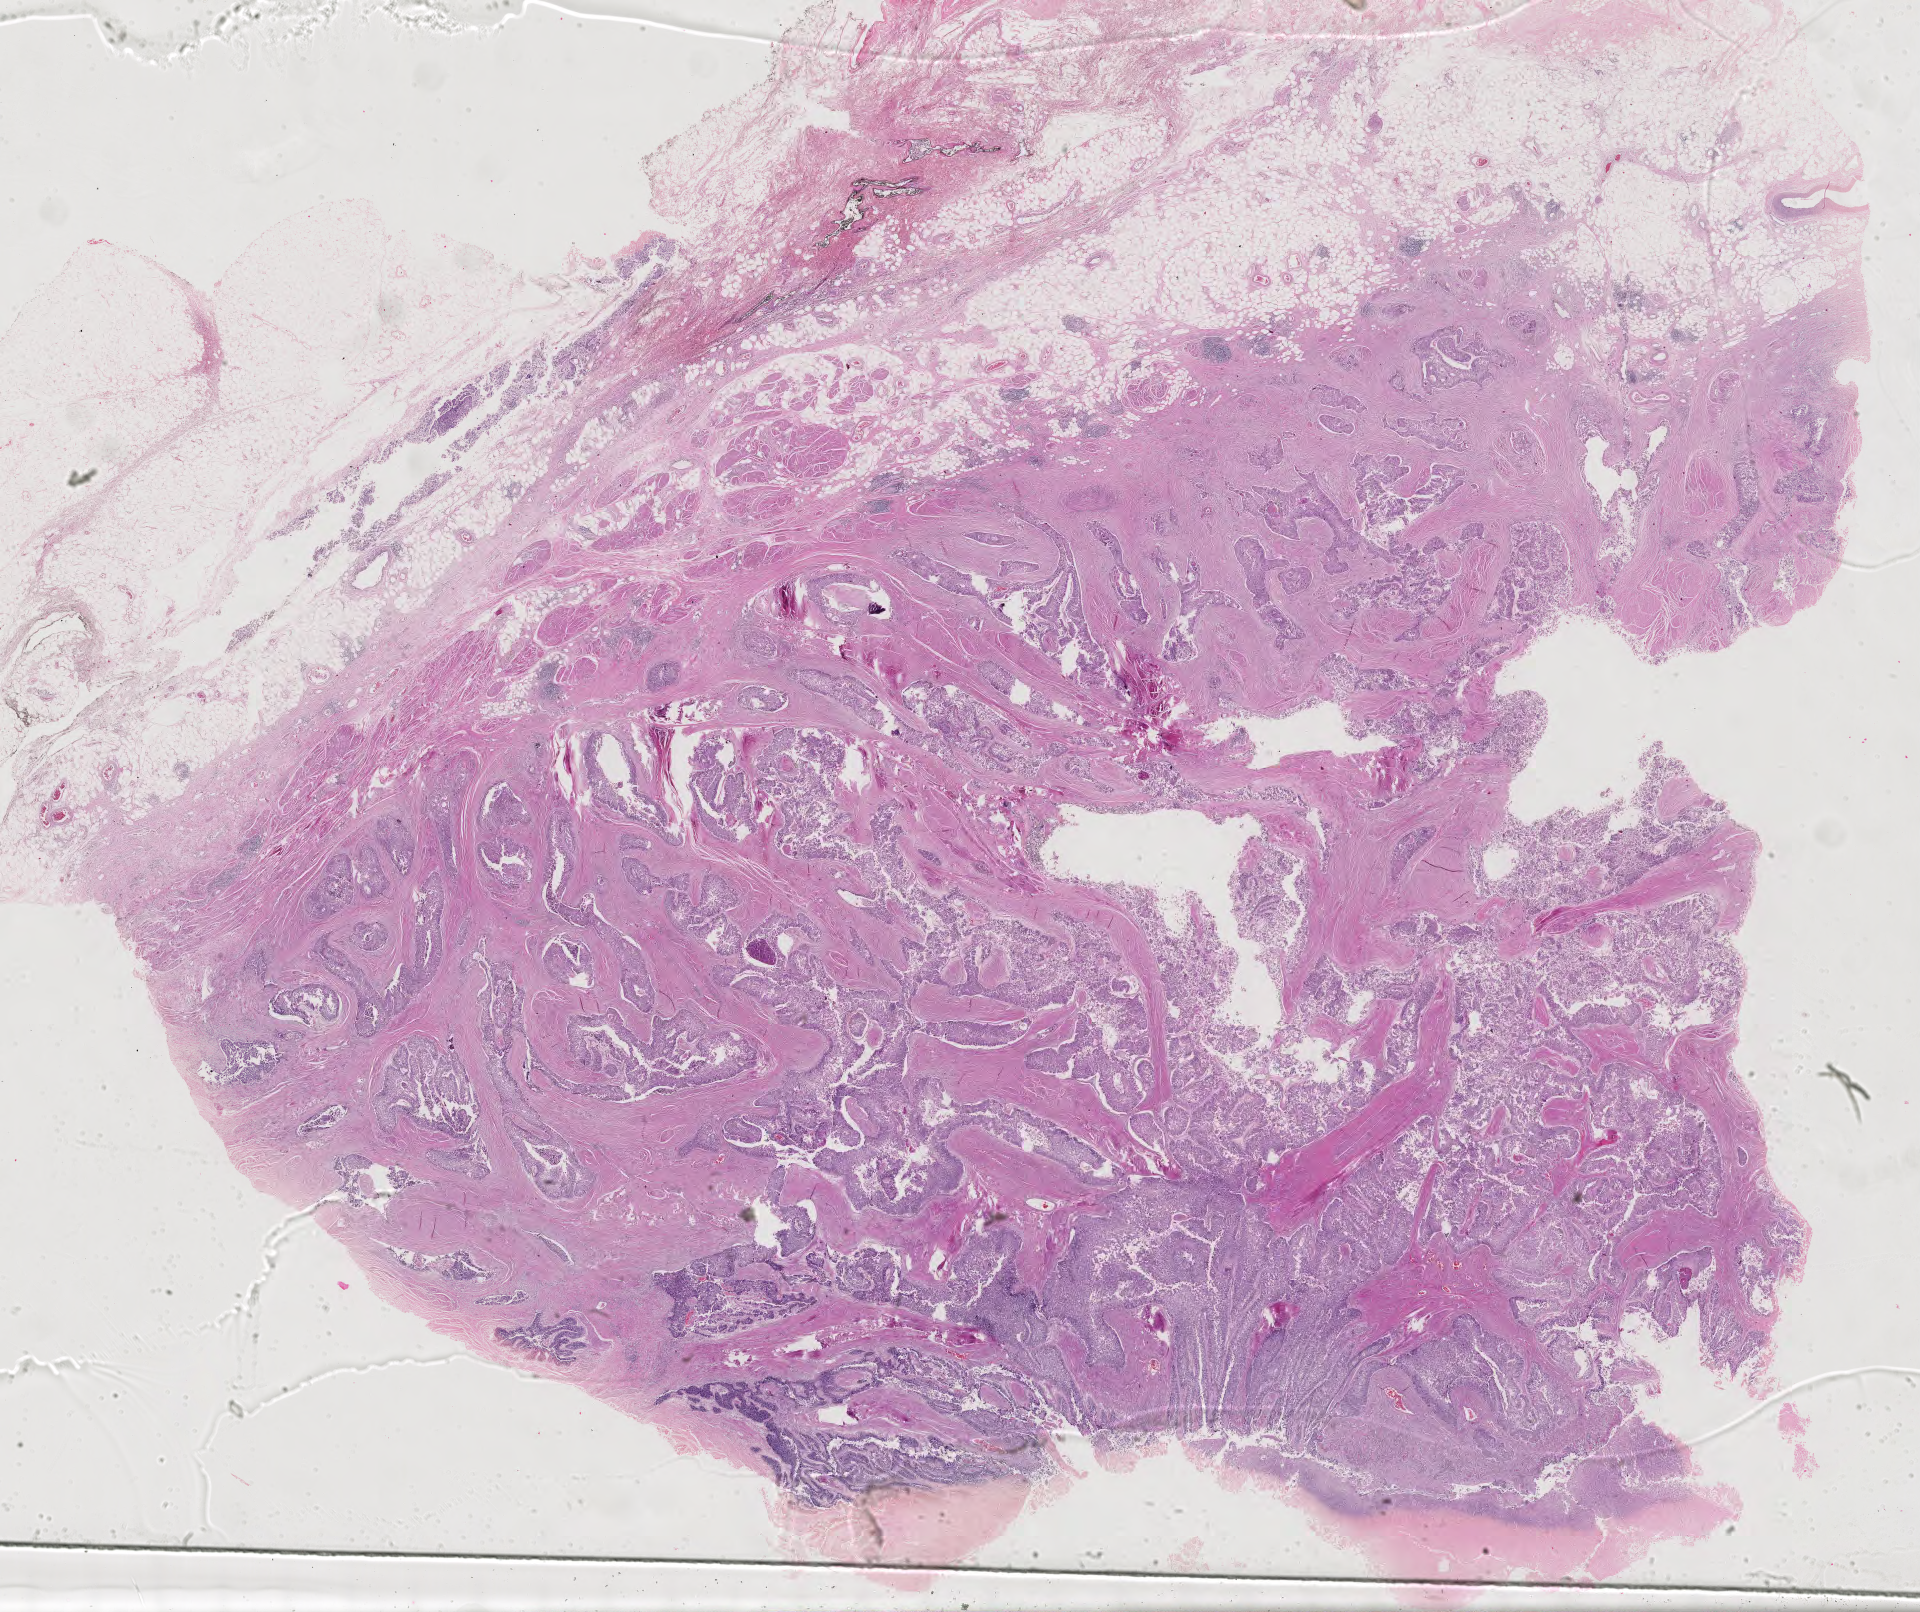
Digitized H&E-stained tissue section (whole slide) — low-resolution overview of the scanned area, about 28.0 x 23.5 mm, formalin-fixed paraffin-embedded (FFPE) diagnostic section, bladder, primary tumour sample. Patient: female, age at initial diagnosis 59 years. Histologic grade: high grade.
AJCC pathologic stage: III. Pathologic diagnosis: Papillary transitional cell carcinoma.